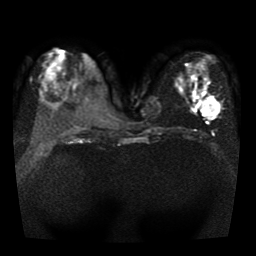
Breast MRI, one axial slice. Slice 17 of 41 in the series (ordered by position). Diffusion-weighted series; image 2 of 4 stored at this slice position (different b-values; order by instance number). 1.5 T. 5 mm slice thickness. 256 × 256 image matrix, field of view 330 × 330 mm. Female patient.
Outlined on this slice (manually delineated by an expert):
- tumour on diffusion-weighted imaging: box from (x=205, y=101) to (x=218, y=116) px